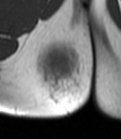
MRI of an extremity soft-tissue mass, one axial slice. Position 15 of 47 along the scan axis. MR volume resampled by the dataset authors to the PET/CT grid (not the native acquisition matrix). 3.27 mm slice thickness. 121 × 139 image matrix, field of view 118 × 136 mm. Female patient. From the clinical record (not read from this slice): histological type: epithelioid sarcoma; grade: intermediate; site of the primary tumour: right buttock.
Annotated regions visible in this slice (expert contour drawn on MRI and transferred to this co-registered scan by the dataset authors):
- gross tumour volume including surrounding oedema: bounding box <34,39,92,112> (left, top, right, bottom; pixels)
- gross tumour volume (mass): <43,50,76,78>